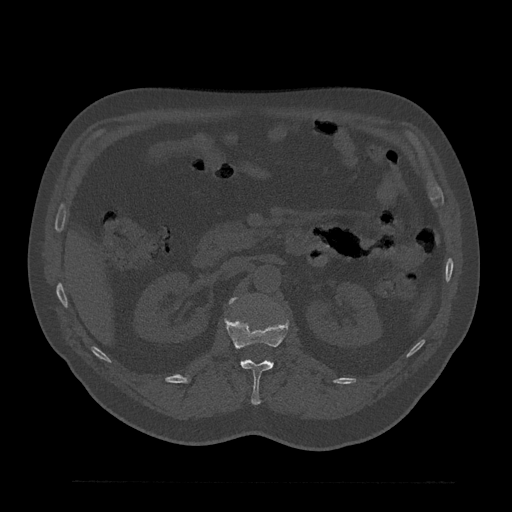
CT including the spine, one axial slice. Reconstruction kernel Br40s/3. 120 kVp. Bone window (W 1800 / L 400 HU). 0.5 mm slice thickness. 512 × 512 image matrix, field of view 430 × 430 mm. Patient: male, 61 years. From the clinical record (not read from this slice): primary cancer: prostate.
Structures marked on this image (semi-automatic segmentation, software-assisted and operator-edited):
- L1 vertebra: box from (x=225, y=318) to (x=289, y=405) px
- L2 vertebra: (x=230, y=298)–(x=235, y=303)